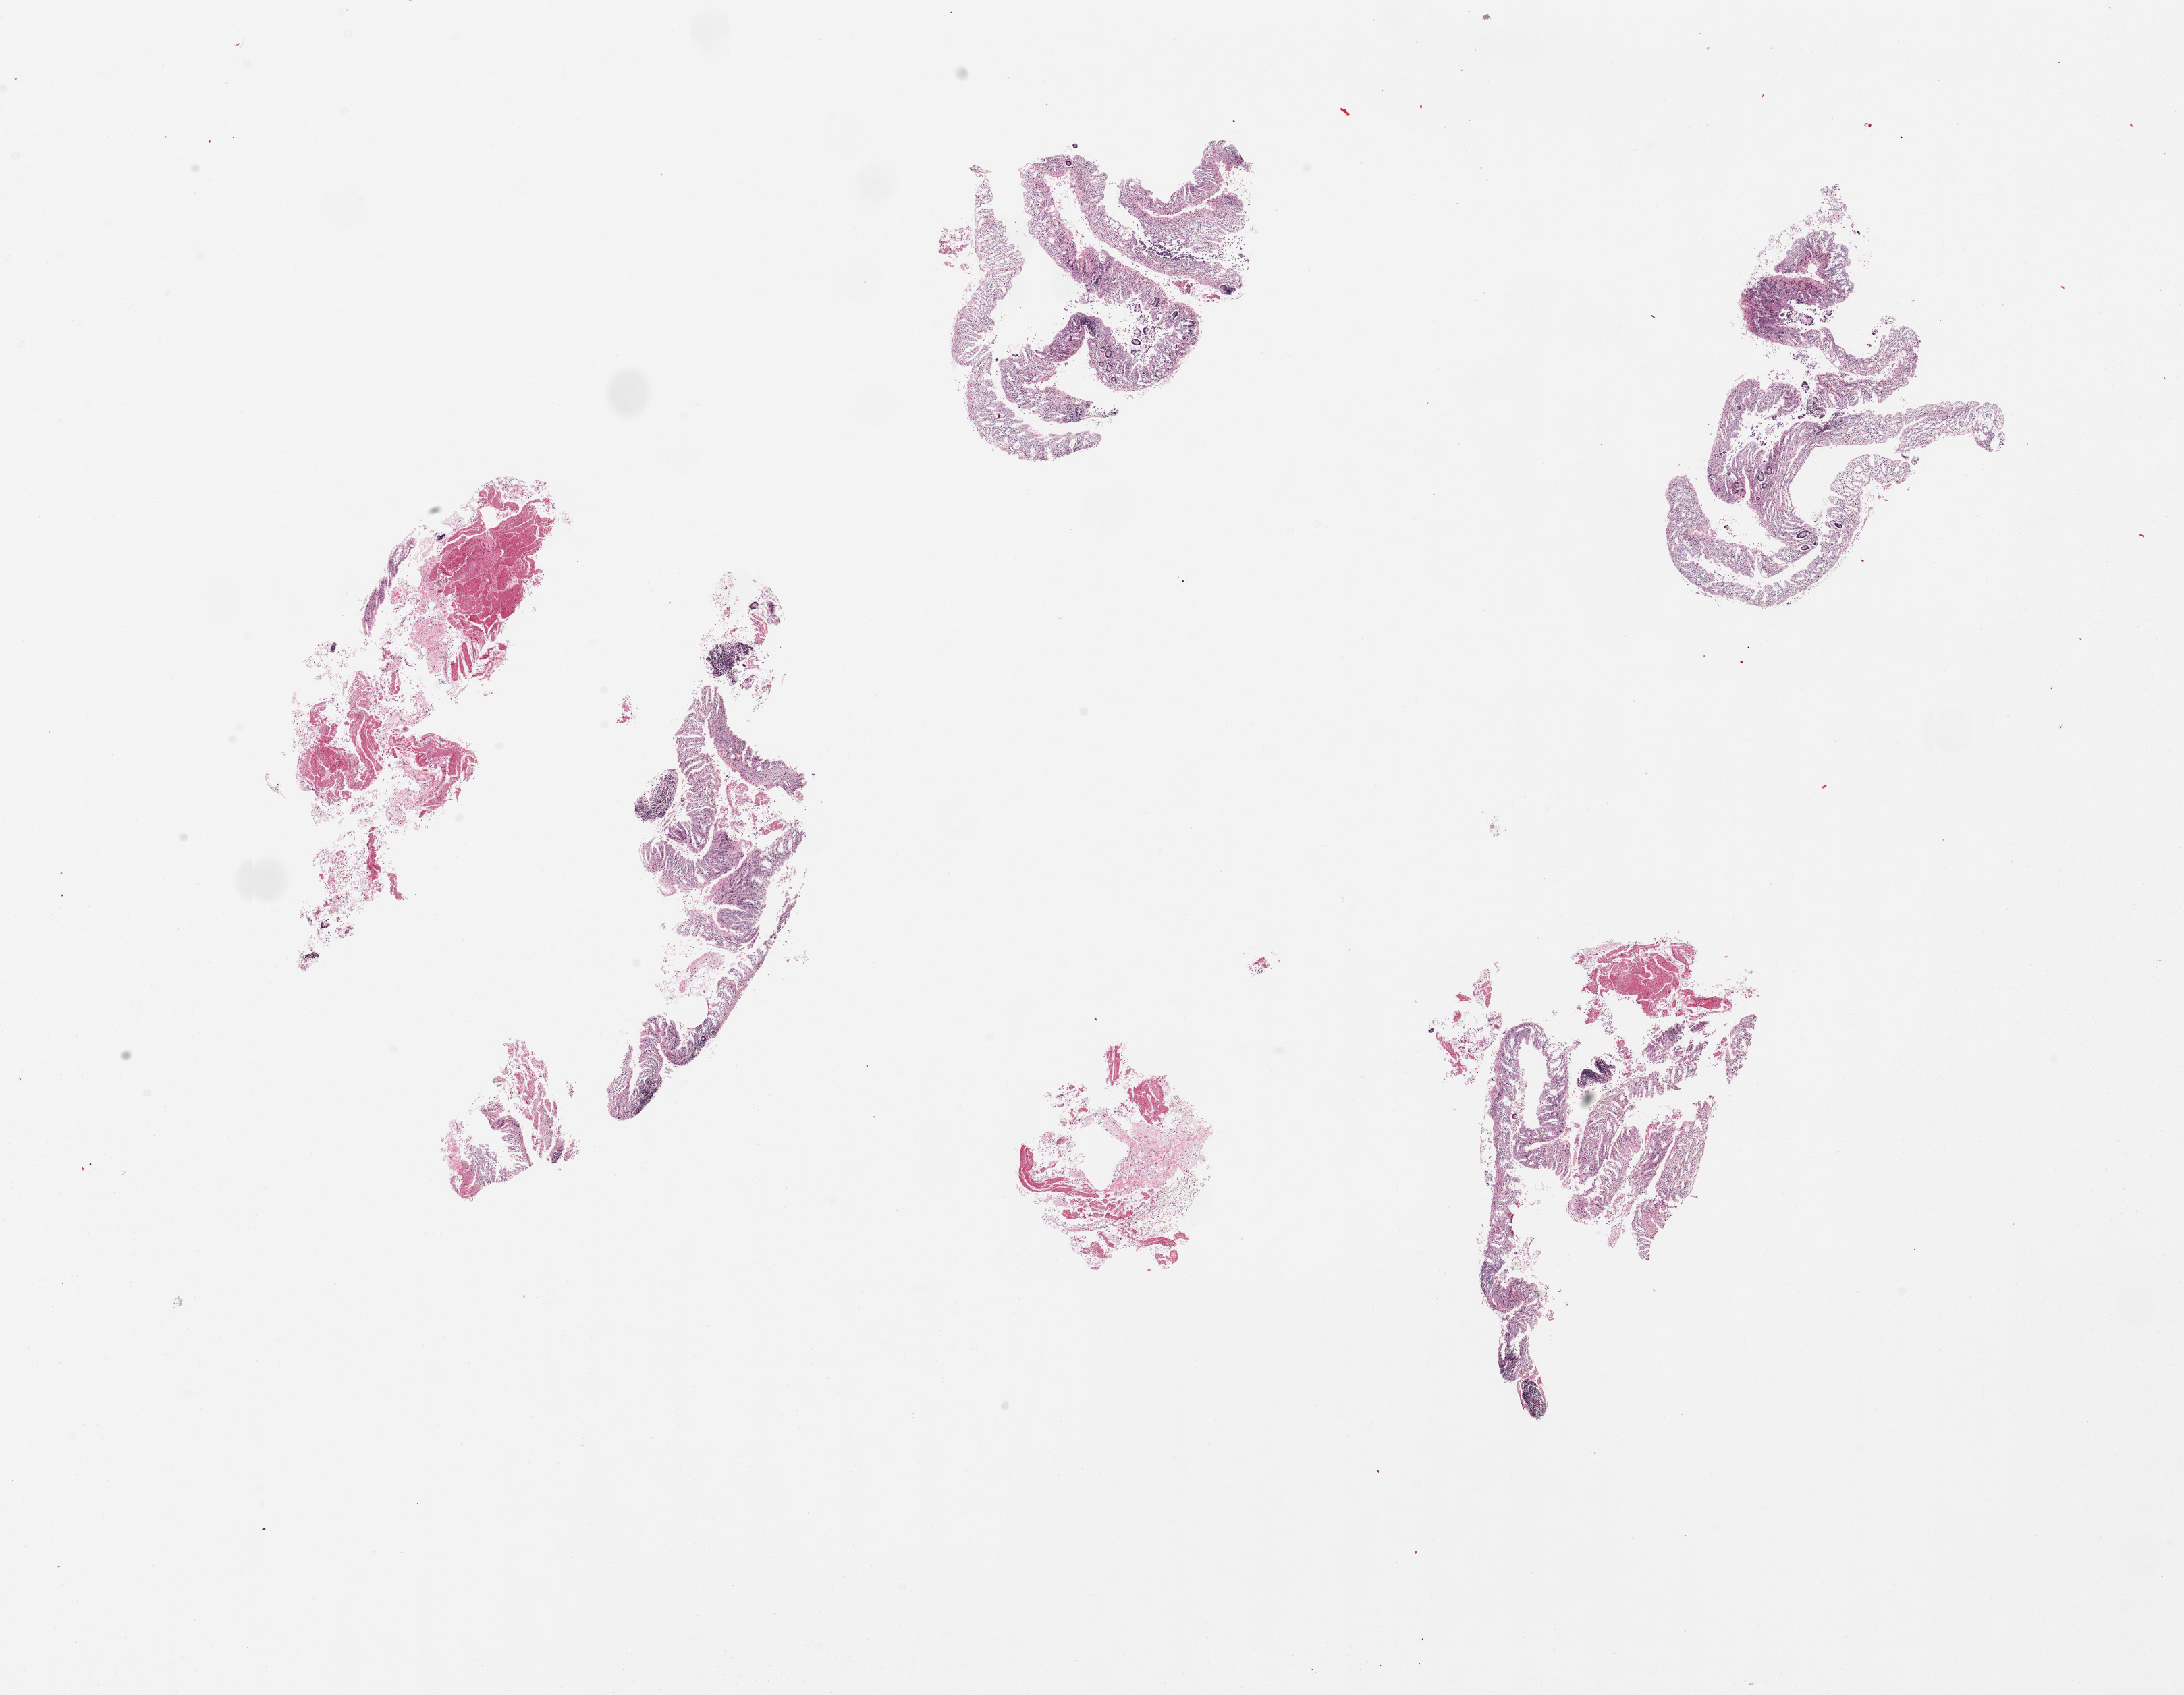
Whole-slide image, haematoxylin and eosin stain, shown as a low-resolution overview of the whole scanned area (about 25.6 x 19.9 mm, acquisition: 20x scan), PAXgene-fixed paraffin-embedded (PFPE) section, section of ileum (target tissue), tissue donor sample. Donor sex: female.
Reviewer comment on this tissue sample: 6 pieces, essentially pure aggregates of mucosa but badly autolyzed; ~10% lymphoid elements.